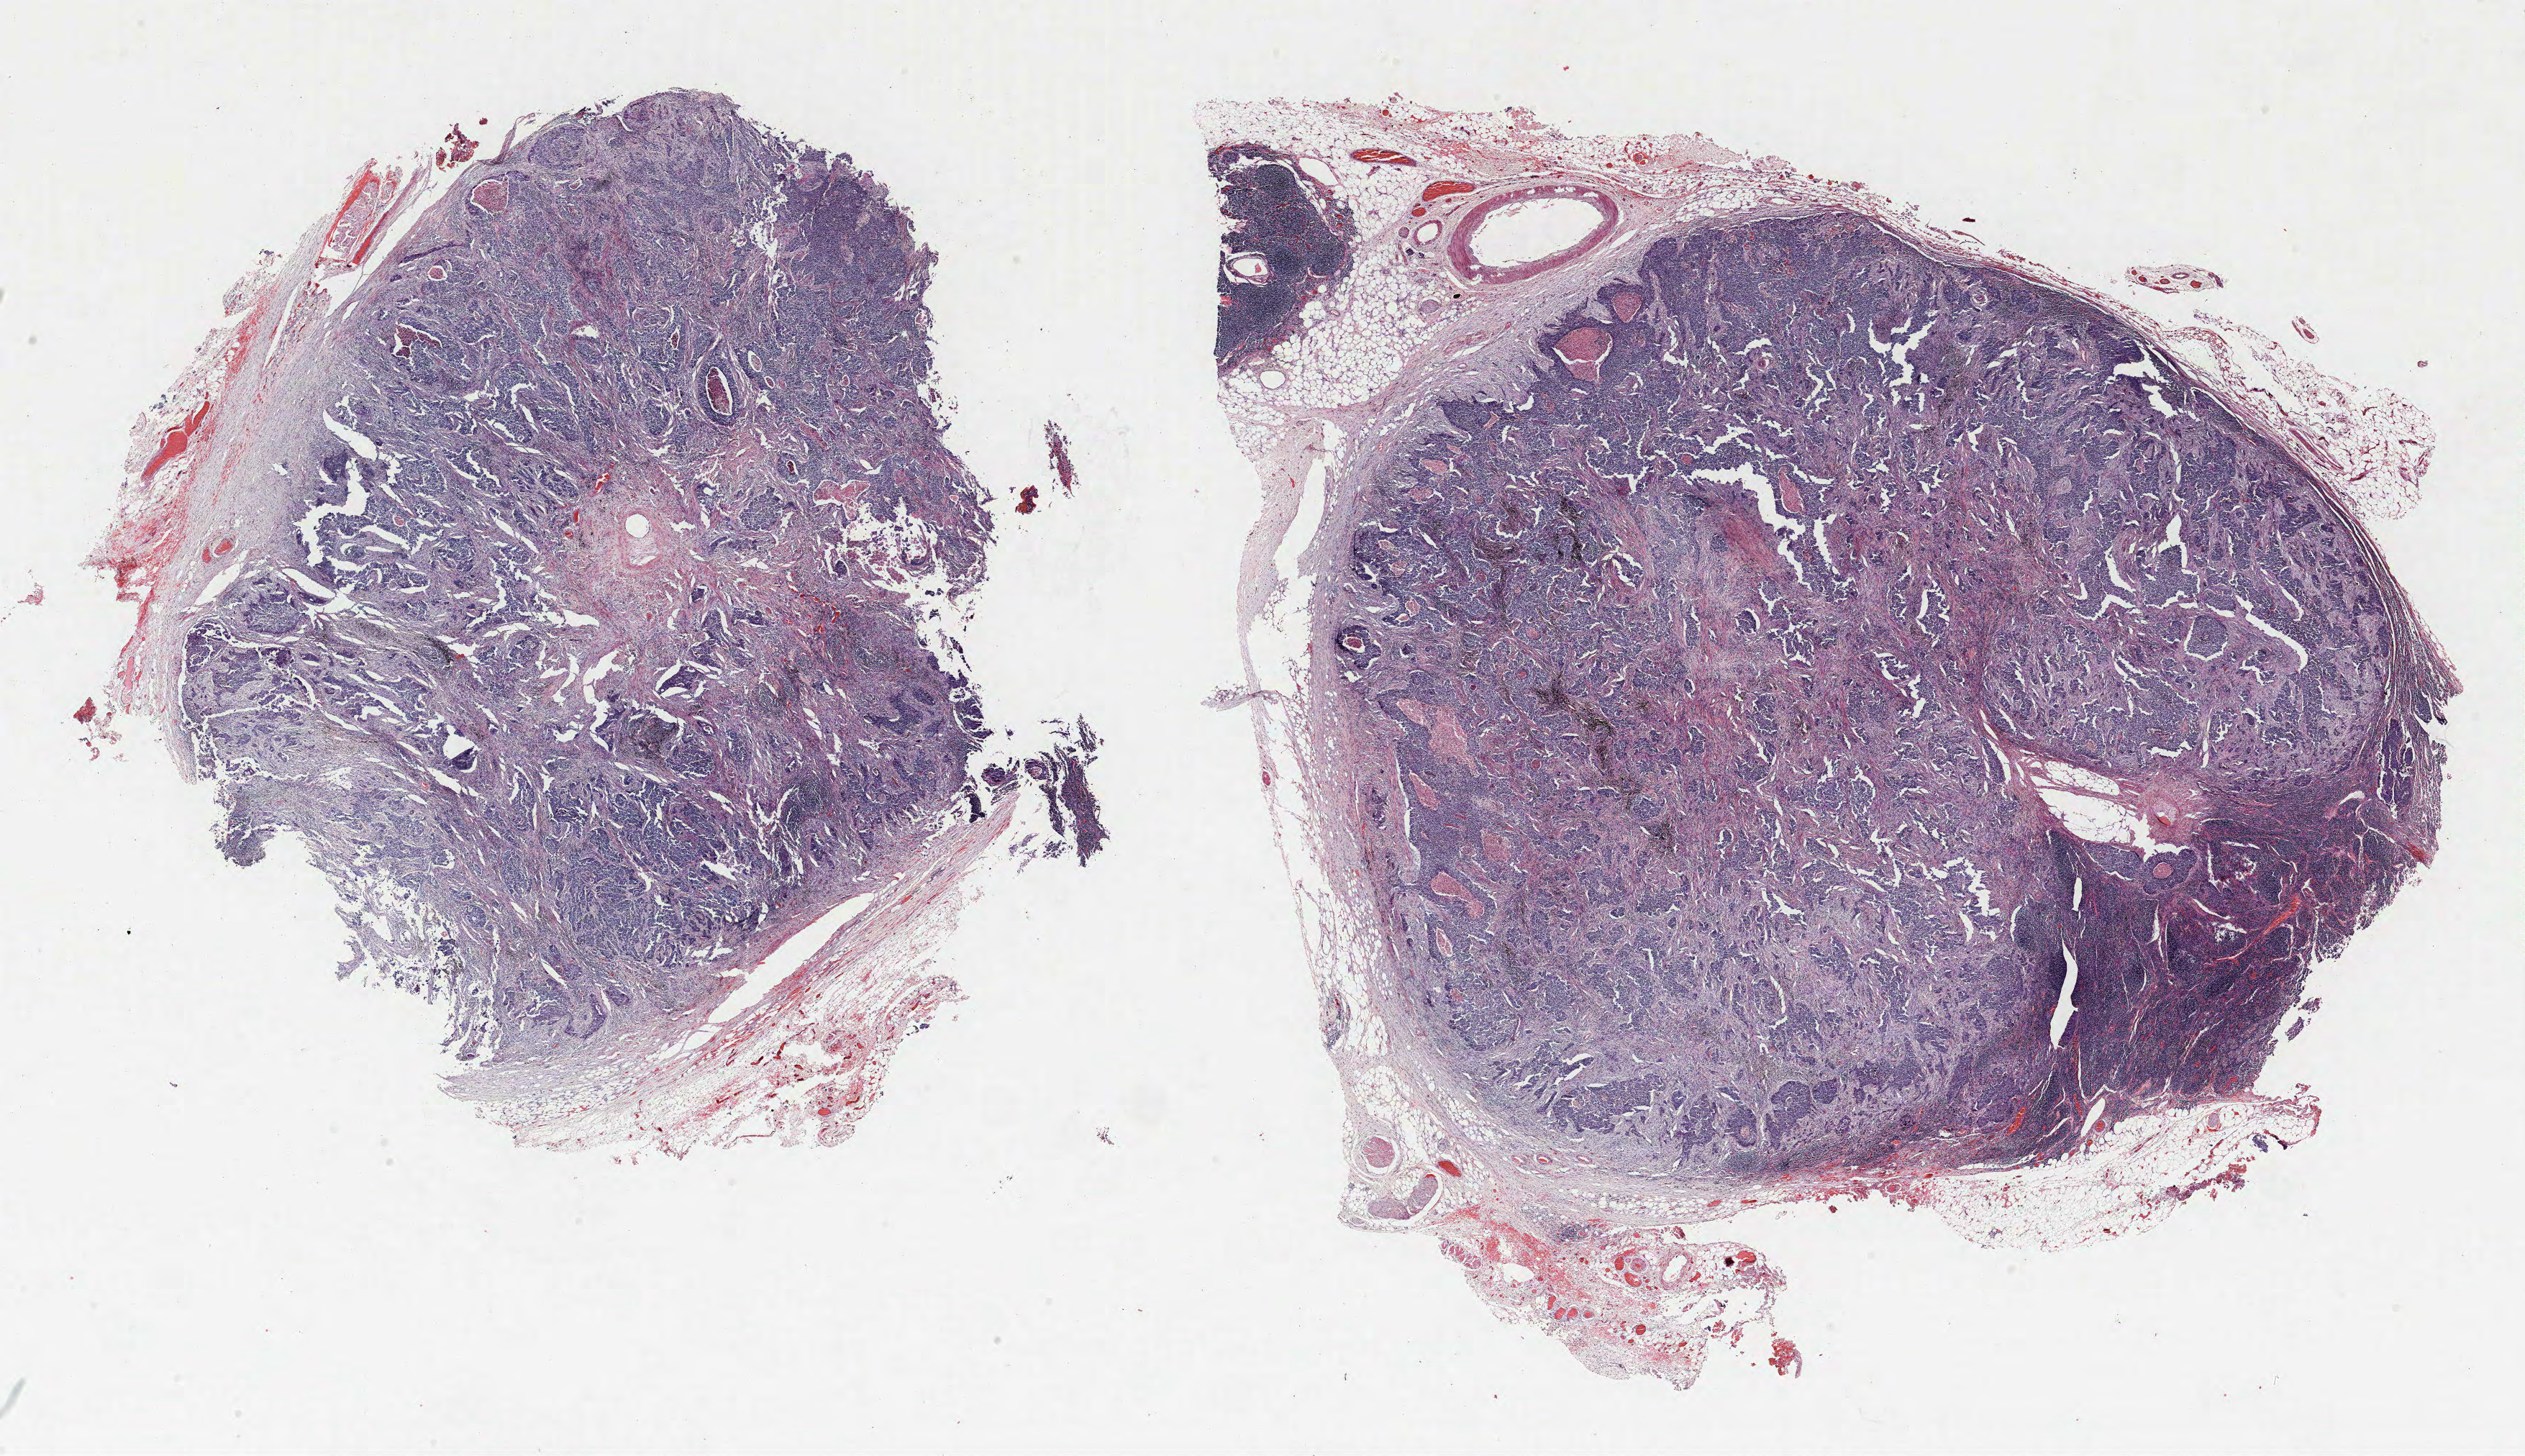
Whole-slide histology image, H&E-stained — shown as a low-resolution overview of the whole scanned area (about 28.1 x 16.2 mm); formalin-fixed paraffin-embedded (FFPE) section; lung tissue. Male, age 64 at enrolment. Current smoker at enrolment. Grade: poorly differentiated (G3).
Tumour size (pathology): 20 mm. Primary tumour location (clinical record): right middle lobe. ICD-O-3 topography: middle lobe of lung (C34.2). Stage (AJCC 6th edition): IIIA. Participant's lung-cancer diagnosis: Non-small cell carcinoma.